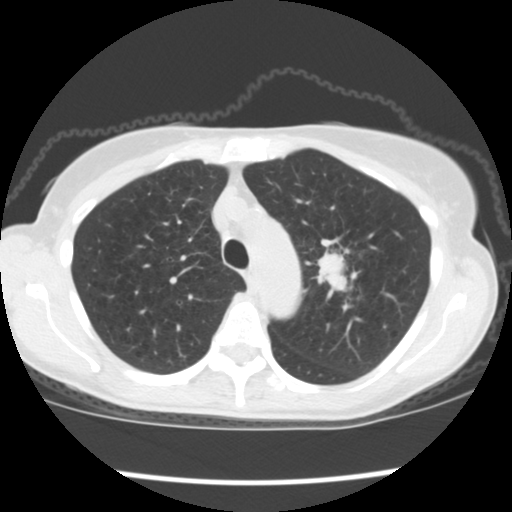
Low-dose screening chest CT, one axial slice; slice 137 of 176 in the series (ordered by position); lung window (W 1500 / L -600 HU); 2.5 mm slice thickness; 512 × 512 image matrix, field of view 318 × 318 mm.
Outlined on this slice (outlined manually by an expert reader):
- lesion 1 (tumor, upper lobe of left lung): bounding box (x1, y1, x2, y2) in pixels: (317, 252, 358, 298)